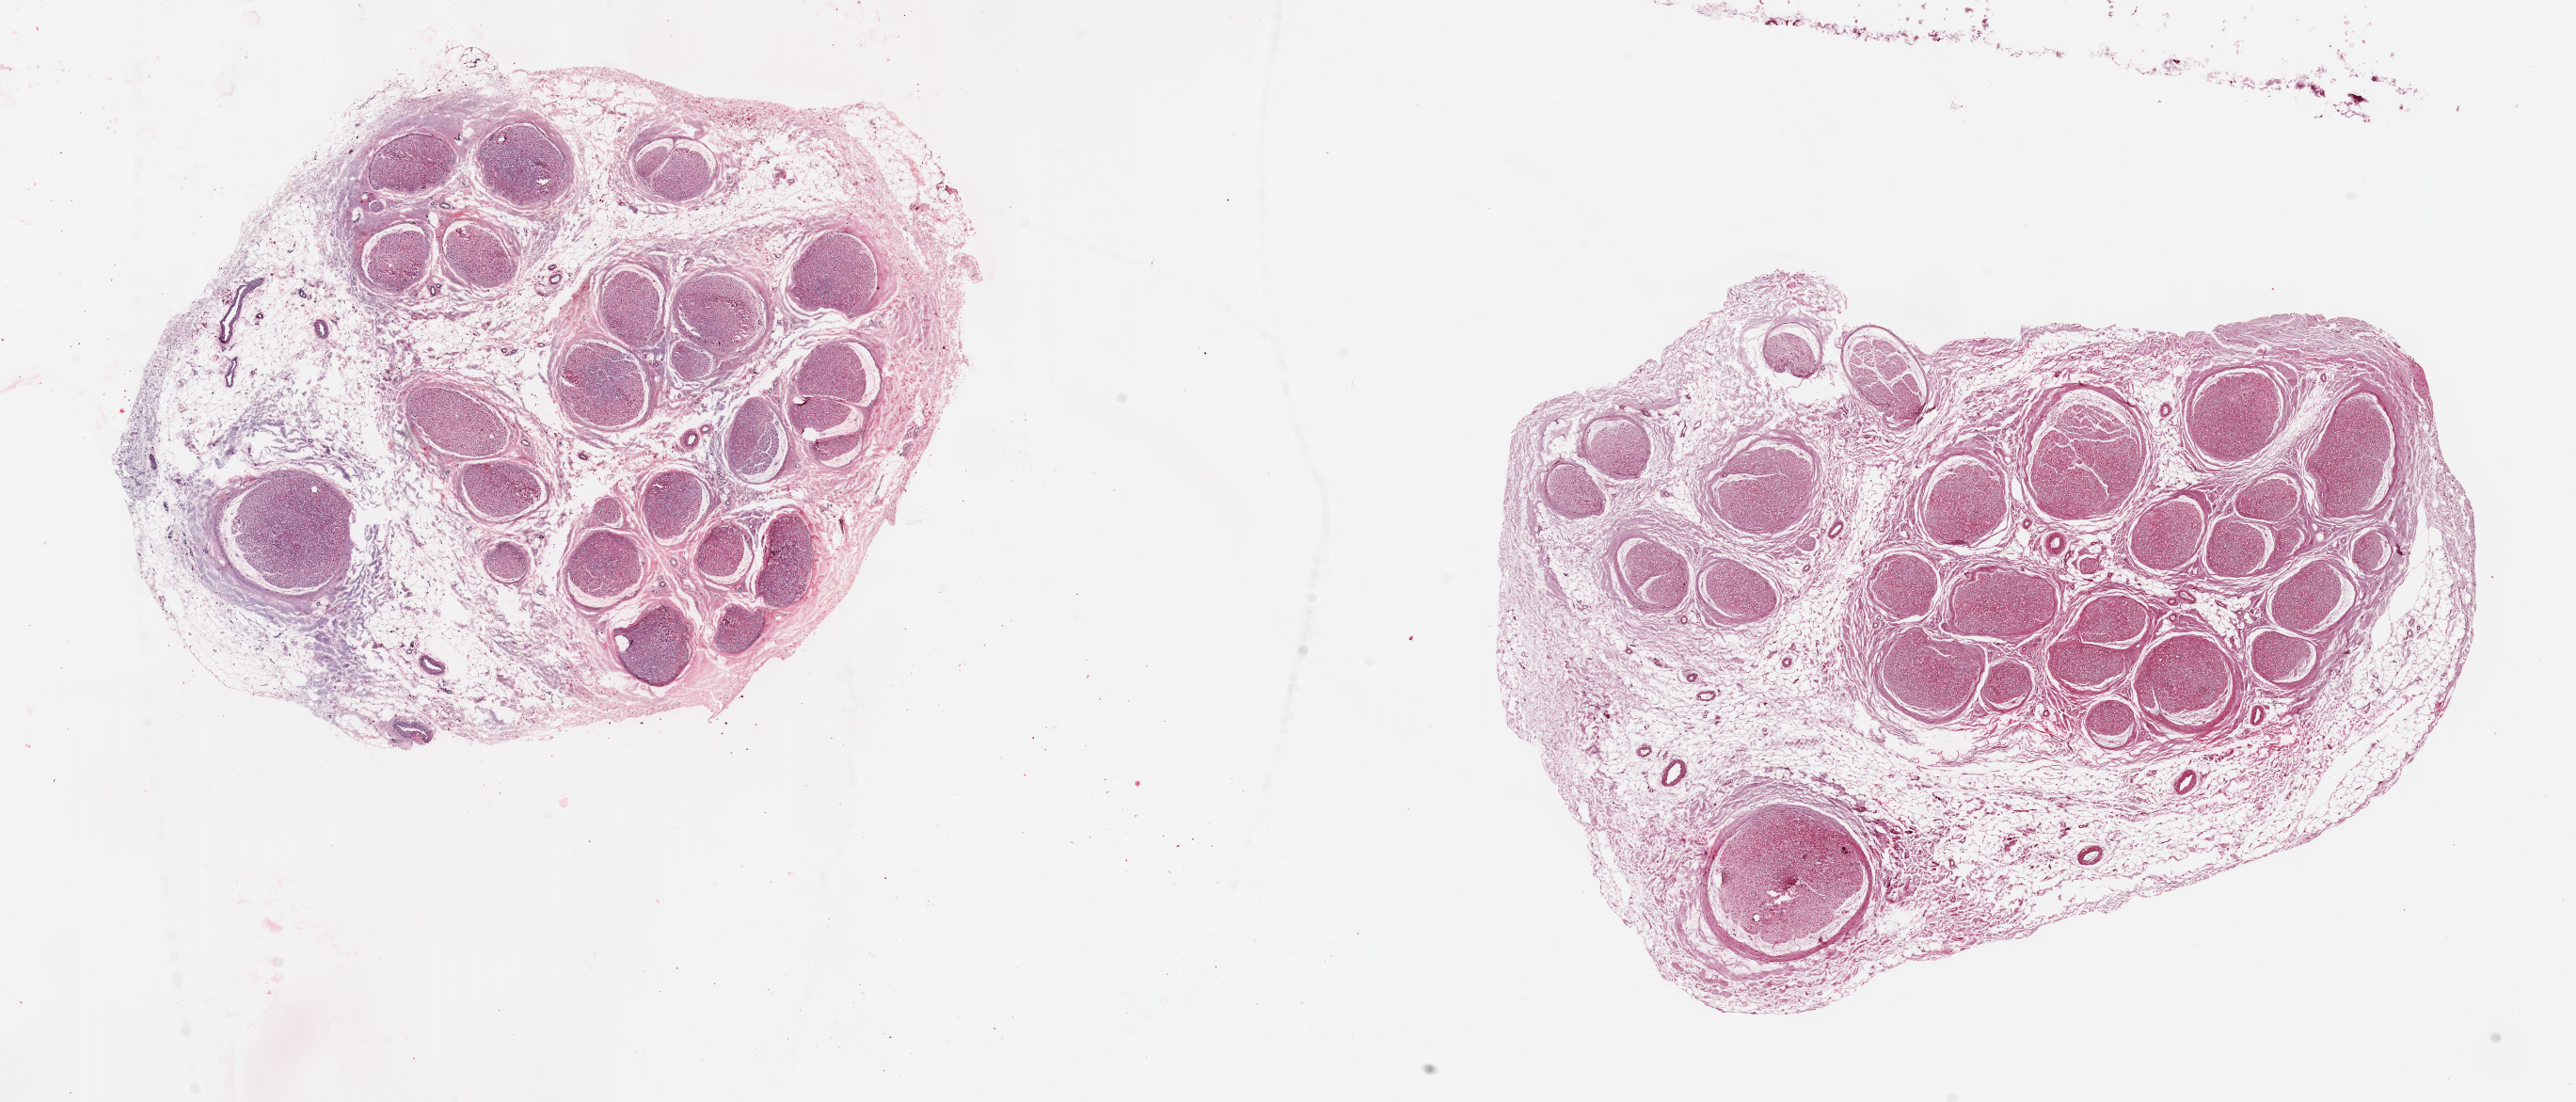
Haematoxylin and eosin whole-slide image, brightfield — a low-resolution overview of the entire scanned area, about 21.7 x 9.3 mm (from a 20x scan); PAXgene-fixed paraffin-embedded (PFPE) section; target tissue: tibial nerve; donor tissue sample. Donor sex: male.
Reviewer comment on this tissue sample: 2 pieces ~7mm d, 60% interstital fat amongst nerve bundles.